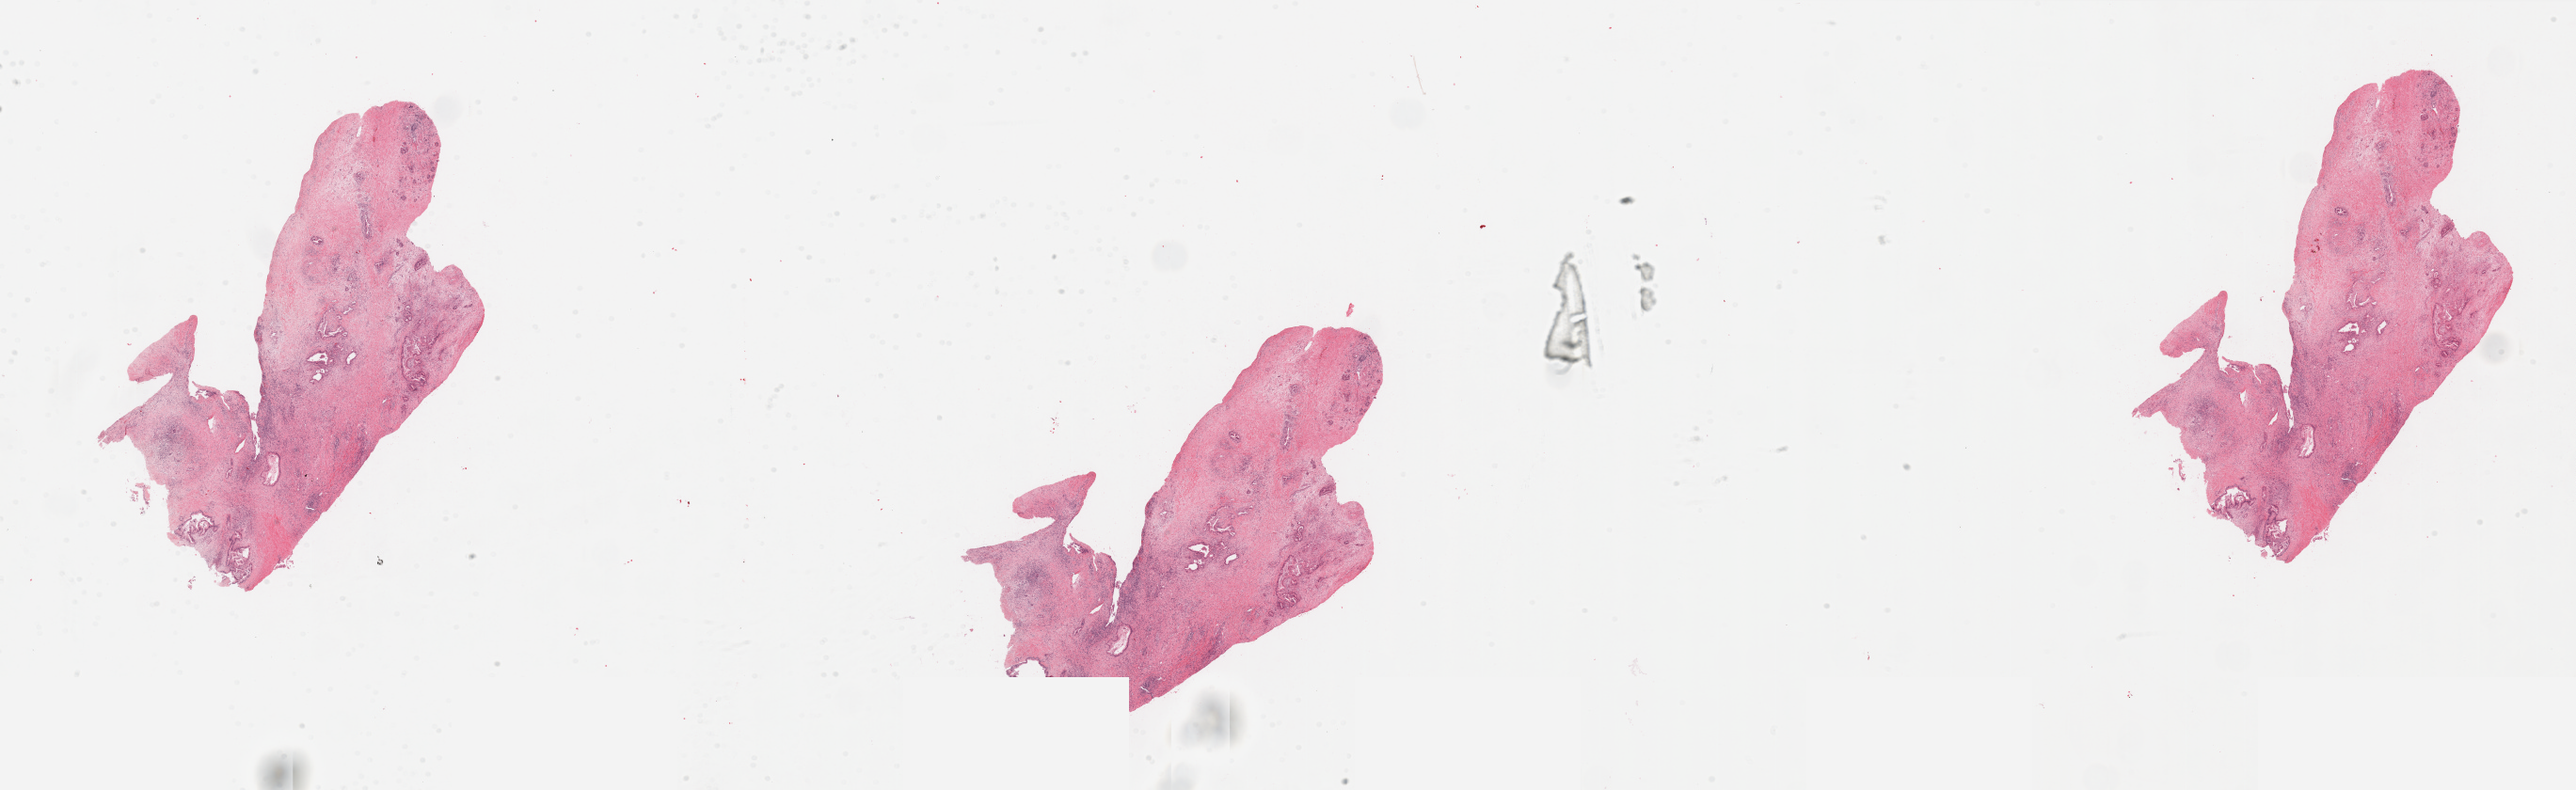
Hematoxylin and eosin (H&E) stained whole-slide image, low-resolution overview of the scanned area, about 43.3 x 13.3 mm (slide scanned at 20x); pancreas, tumour tissue. Patient: male, age 55 years. Histologic grade: G2 (moderately differentiated).
Histologic diagnosis: Infiltrating duct carcinoma, NOS. Primary tumour site (as recorded): body. AJCC pathologic stage: IIB.